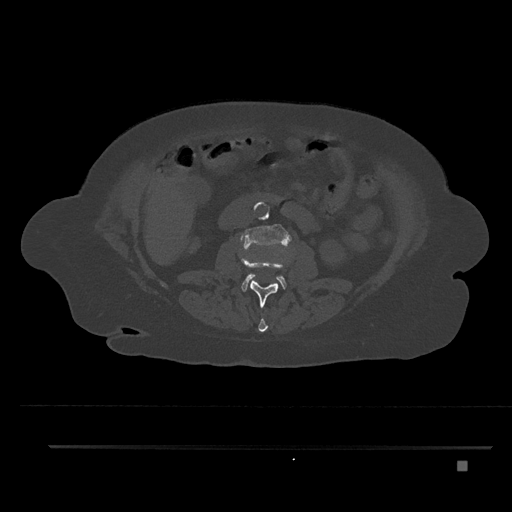
CT including the spine, one axial slice. Slice 163 of 797 in the series (ordered by position). Bone window (W 1800 / L 400 HU). 0.5 mm slice thickness. 512 × 512 image matrix. Patient: female, 76 years. From the clinical record (not read from this slice): primary cancer: lung; vertebrae with lytic lesions (as recorded): T11, L3.
Annotated regions visible in this slice (semi-automatic segmentation, software-assisted and operator-edited):
- L1 vertebra: box from (x=258, y=318) to (x=268, y=332) px
- L2 vertebra: (x=241, y=257)–(x=285, y=308)
- L3 vertebra: (x=241, y=224)–(x=292, y=292)